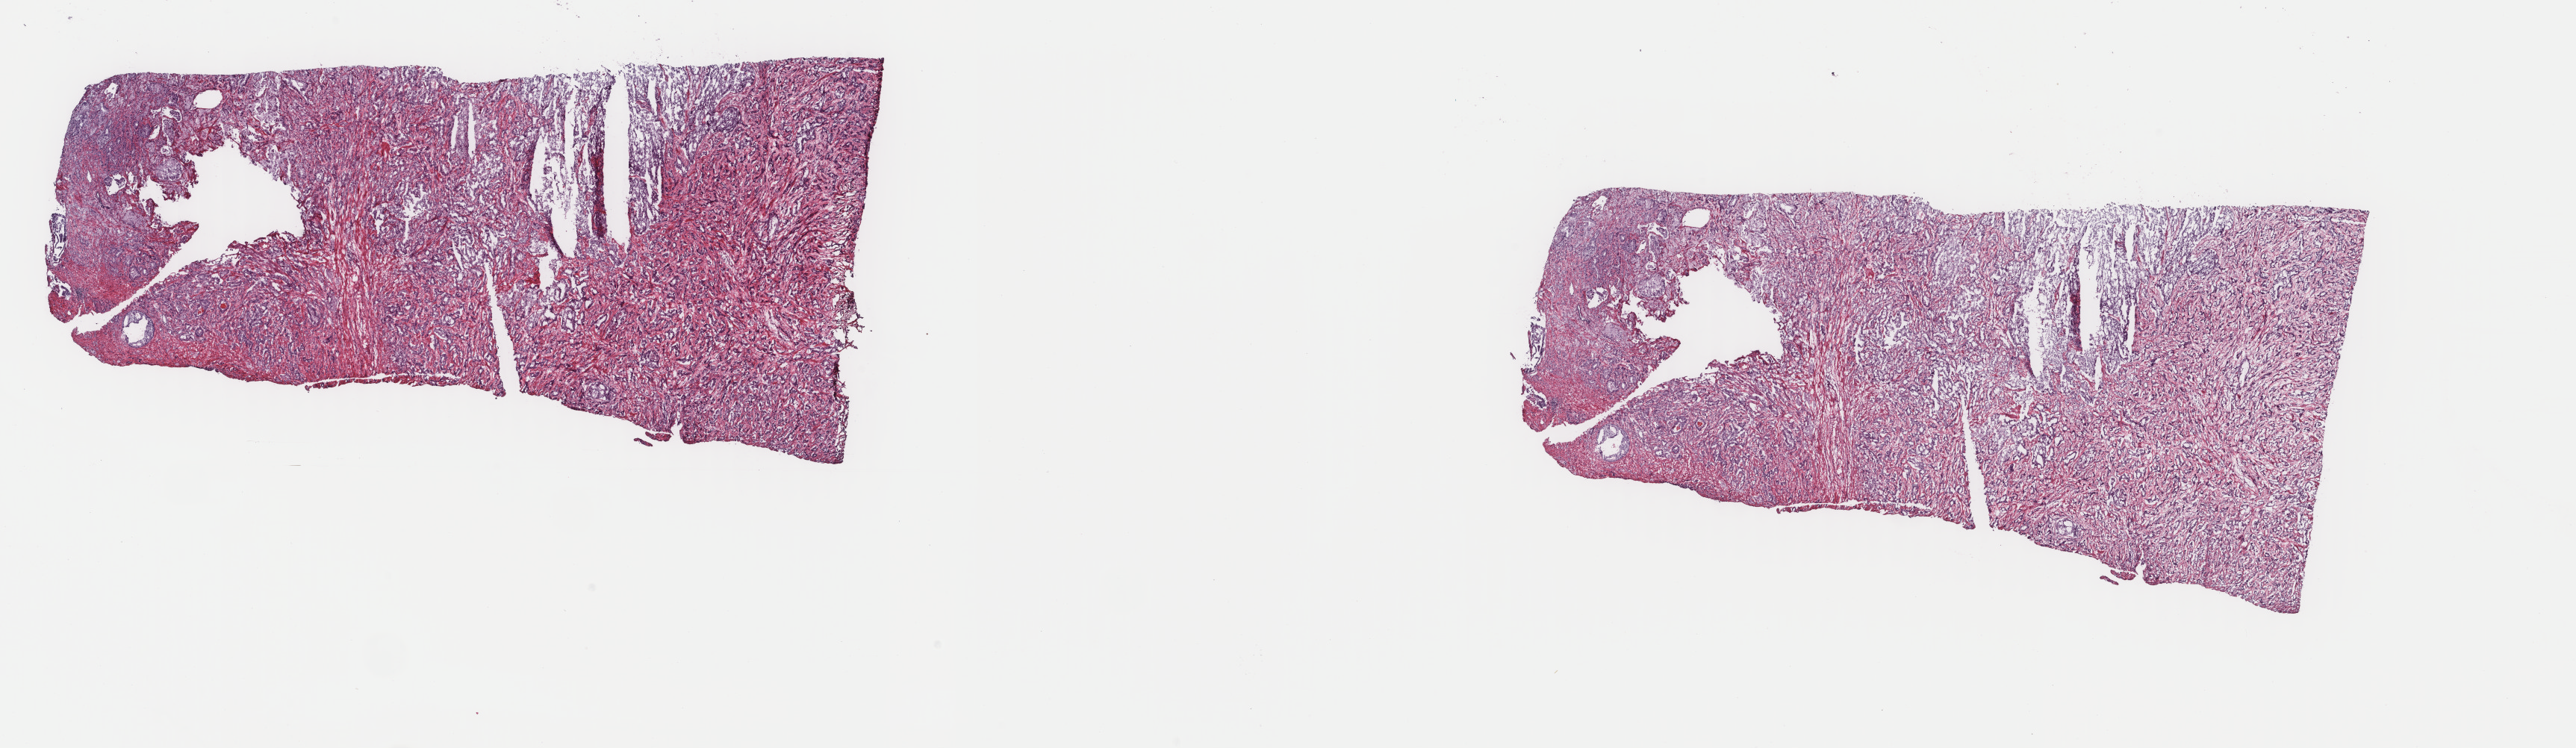
H&E whole-slide image — whole scanned area (about 27.4 x 8.0 mm, slide scanned at 40x) shown as a low-resolution overview; frozen section from the top of the tissue portion; sample: primary tumour, prostate. Male patient; age at initial diagnosis 62 years.
Pathologic diagnosis: Adenocarcinoma, NOS (prostate gland).